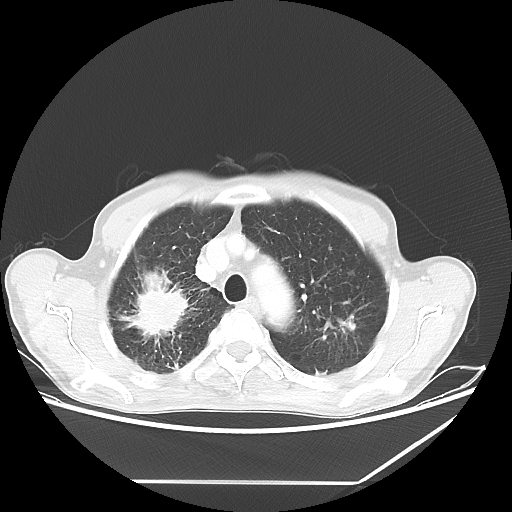
Chest CT, one axial slice; slice 50 of 65 in the series (ordered by position); lung window (W 1500 / L -600 HU); 5 mm slice thickness; 512 × 512 image matrix, field of view 397 × 397 mm. Male patient, age 68 years. Case-level facts recorded for this patient, not image findings: clinical TNM (as recorded): T3 N3 M0.
Annotated regions visible in this slice (bounding box drawn by a radiologist):
- lung tumour (recorded histology: adenocarcinoma): bounding box [x1, y1, x2, y2] px = [116, 261, 189, 350]